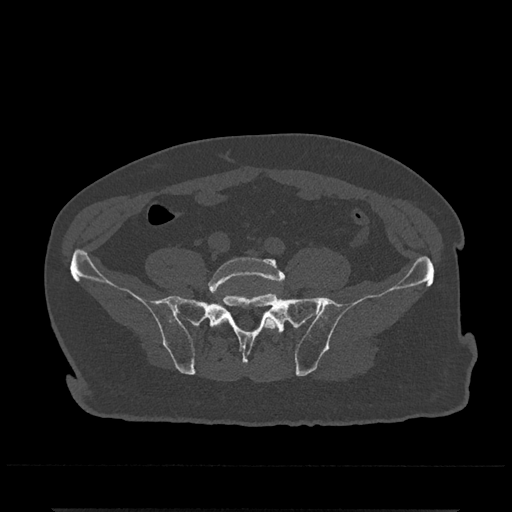
CT including the spine, one axial slice. Position 49 of 797 along the scan axis. Reconstruction kernel Br40s/3. Bone window (W 1800 / L 400 HU). 0.5 mm slice thickness. 512 × 512 image matrix. Patient: male, 67 years. Case-level facts recorded for this patient, not image findings: primary cancer: prostate.
Outlined on this slice (semi-automatic segmentation, software-assisted and operator-edited):
- L5 vertebra: bounding box <209,257,285,331> (left, top, right, bottom; pixels)